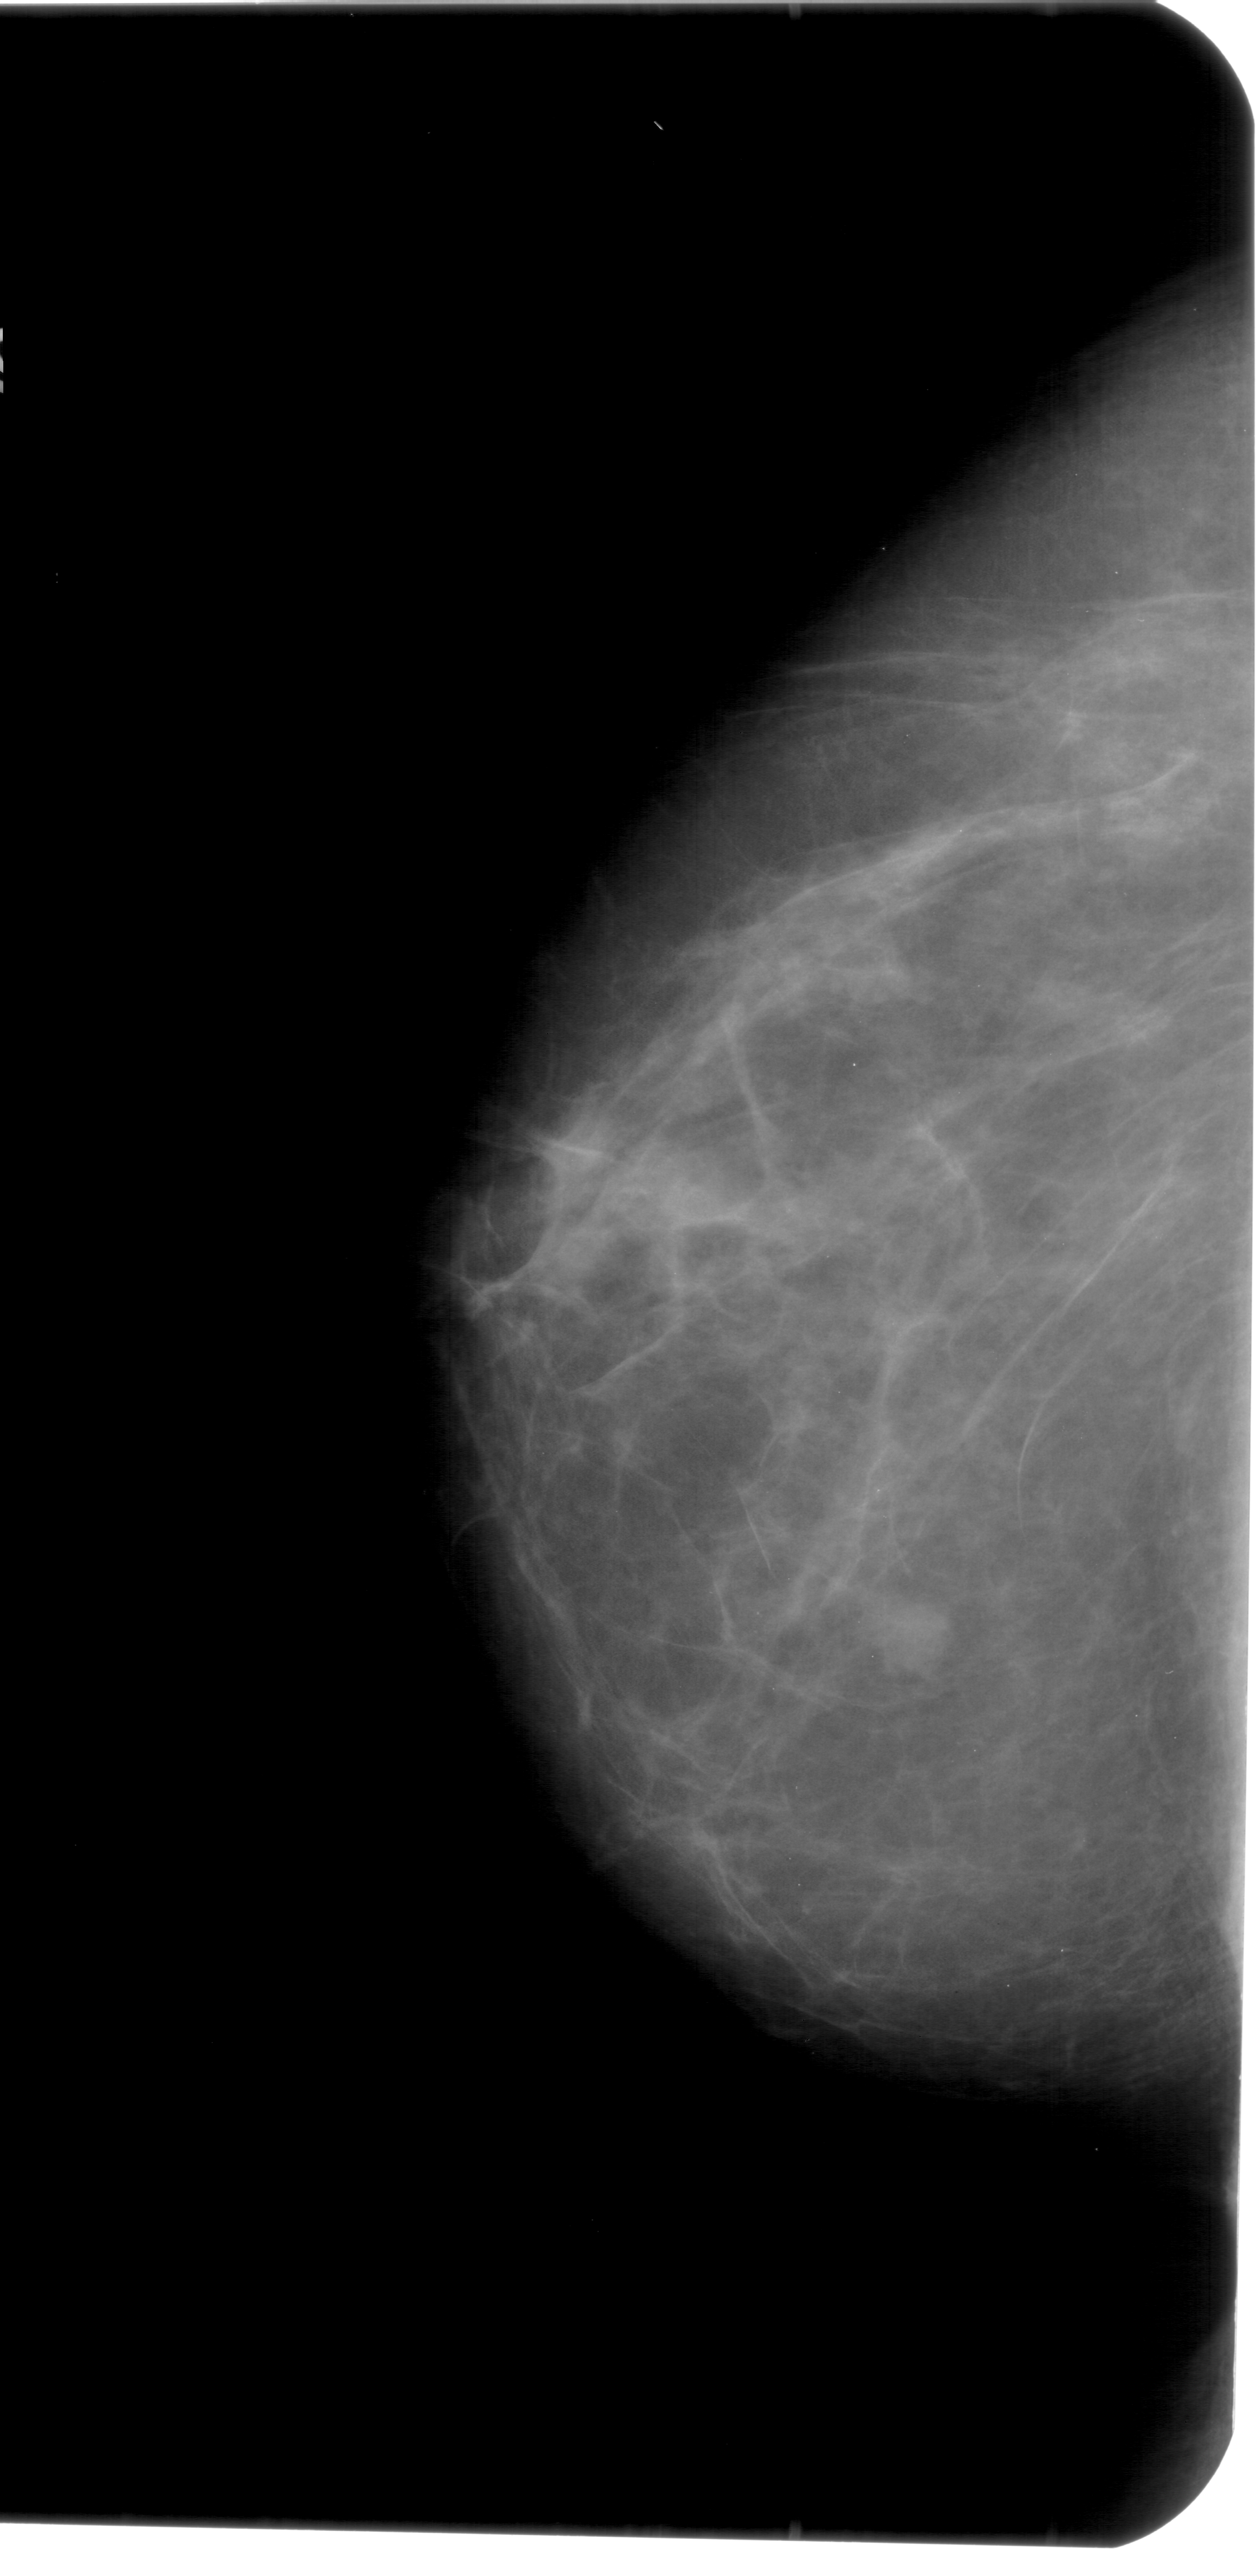
Scanned film-screen mammogram, left breast, CC view.
- Finding: mass, shape irregular, margins ill defined; BI-RADS assessment category 4; pathology result (as recorded, not read from the image): benign.